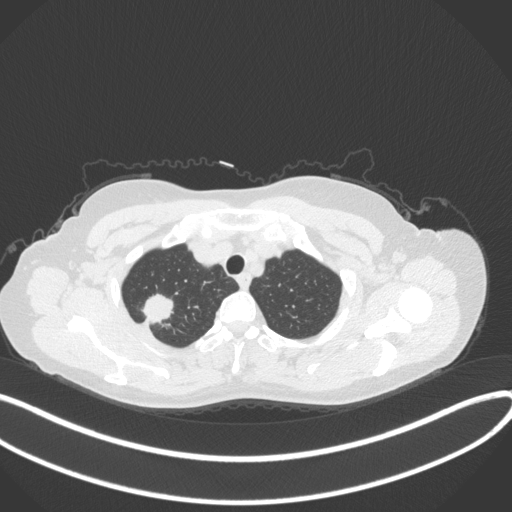
Chest CT, one axial slice. Slice 314 of 342 in the series (ordered by position). Lung window (W 1500 / L -600 HU). 1 mm slice thickness. 512 × 512 image matrix, field of view 400 × 400 mm. Patient: female, 50 years. From the clinical record (not read from this slice): clinical TNM (as recorded): T1c N0 M0; histopathological grade: G2-3.
Annotated regions visible in this slice (bounding box drawn by a radiologist):
- lung tumour (recorded histology: adenocarcinoma): box from (x=139, y=292) to (x=176, y=325) px